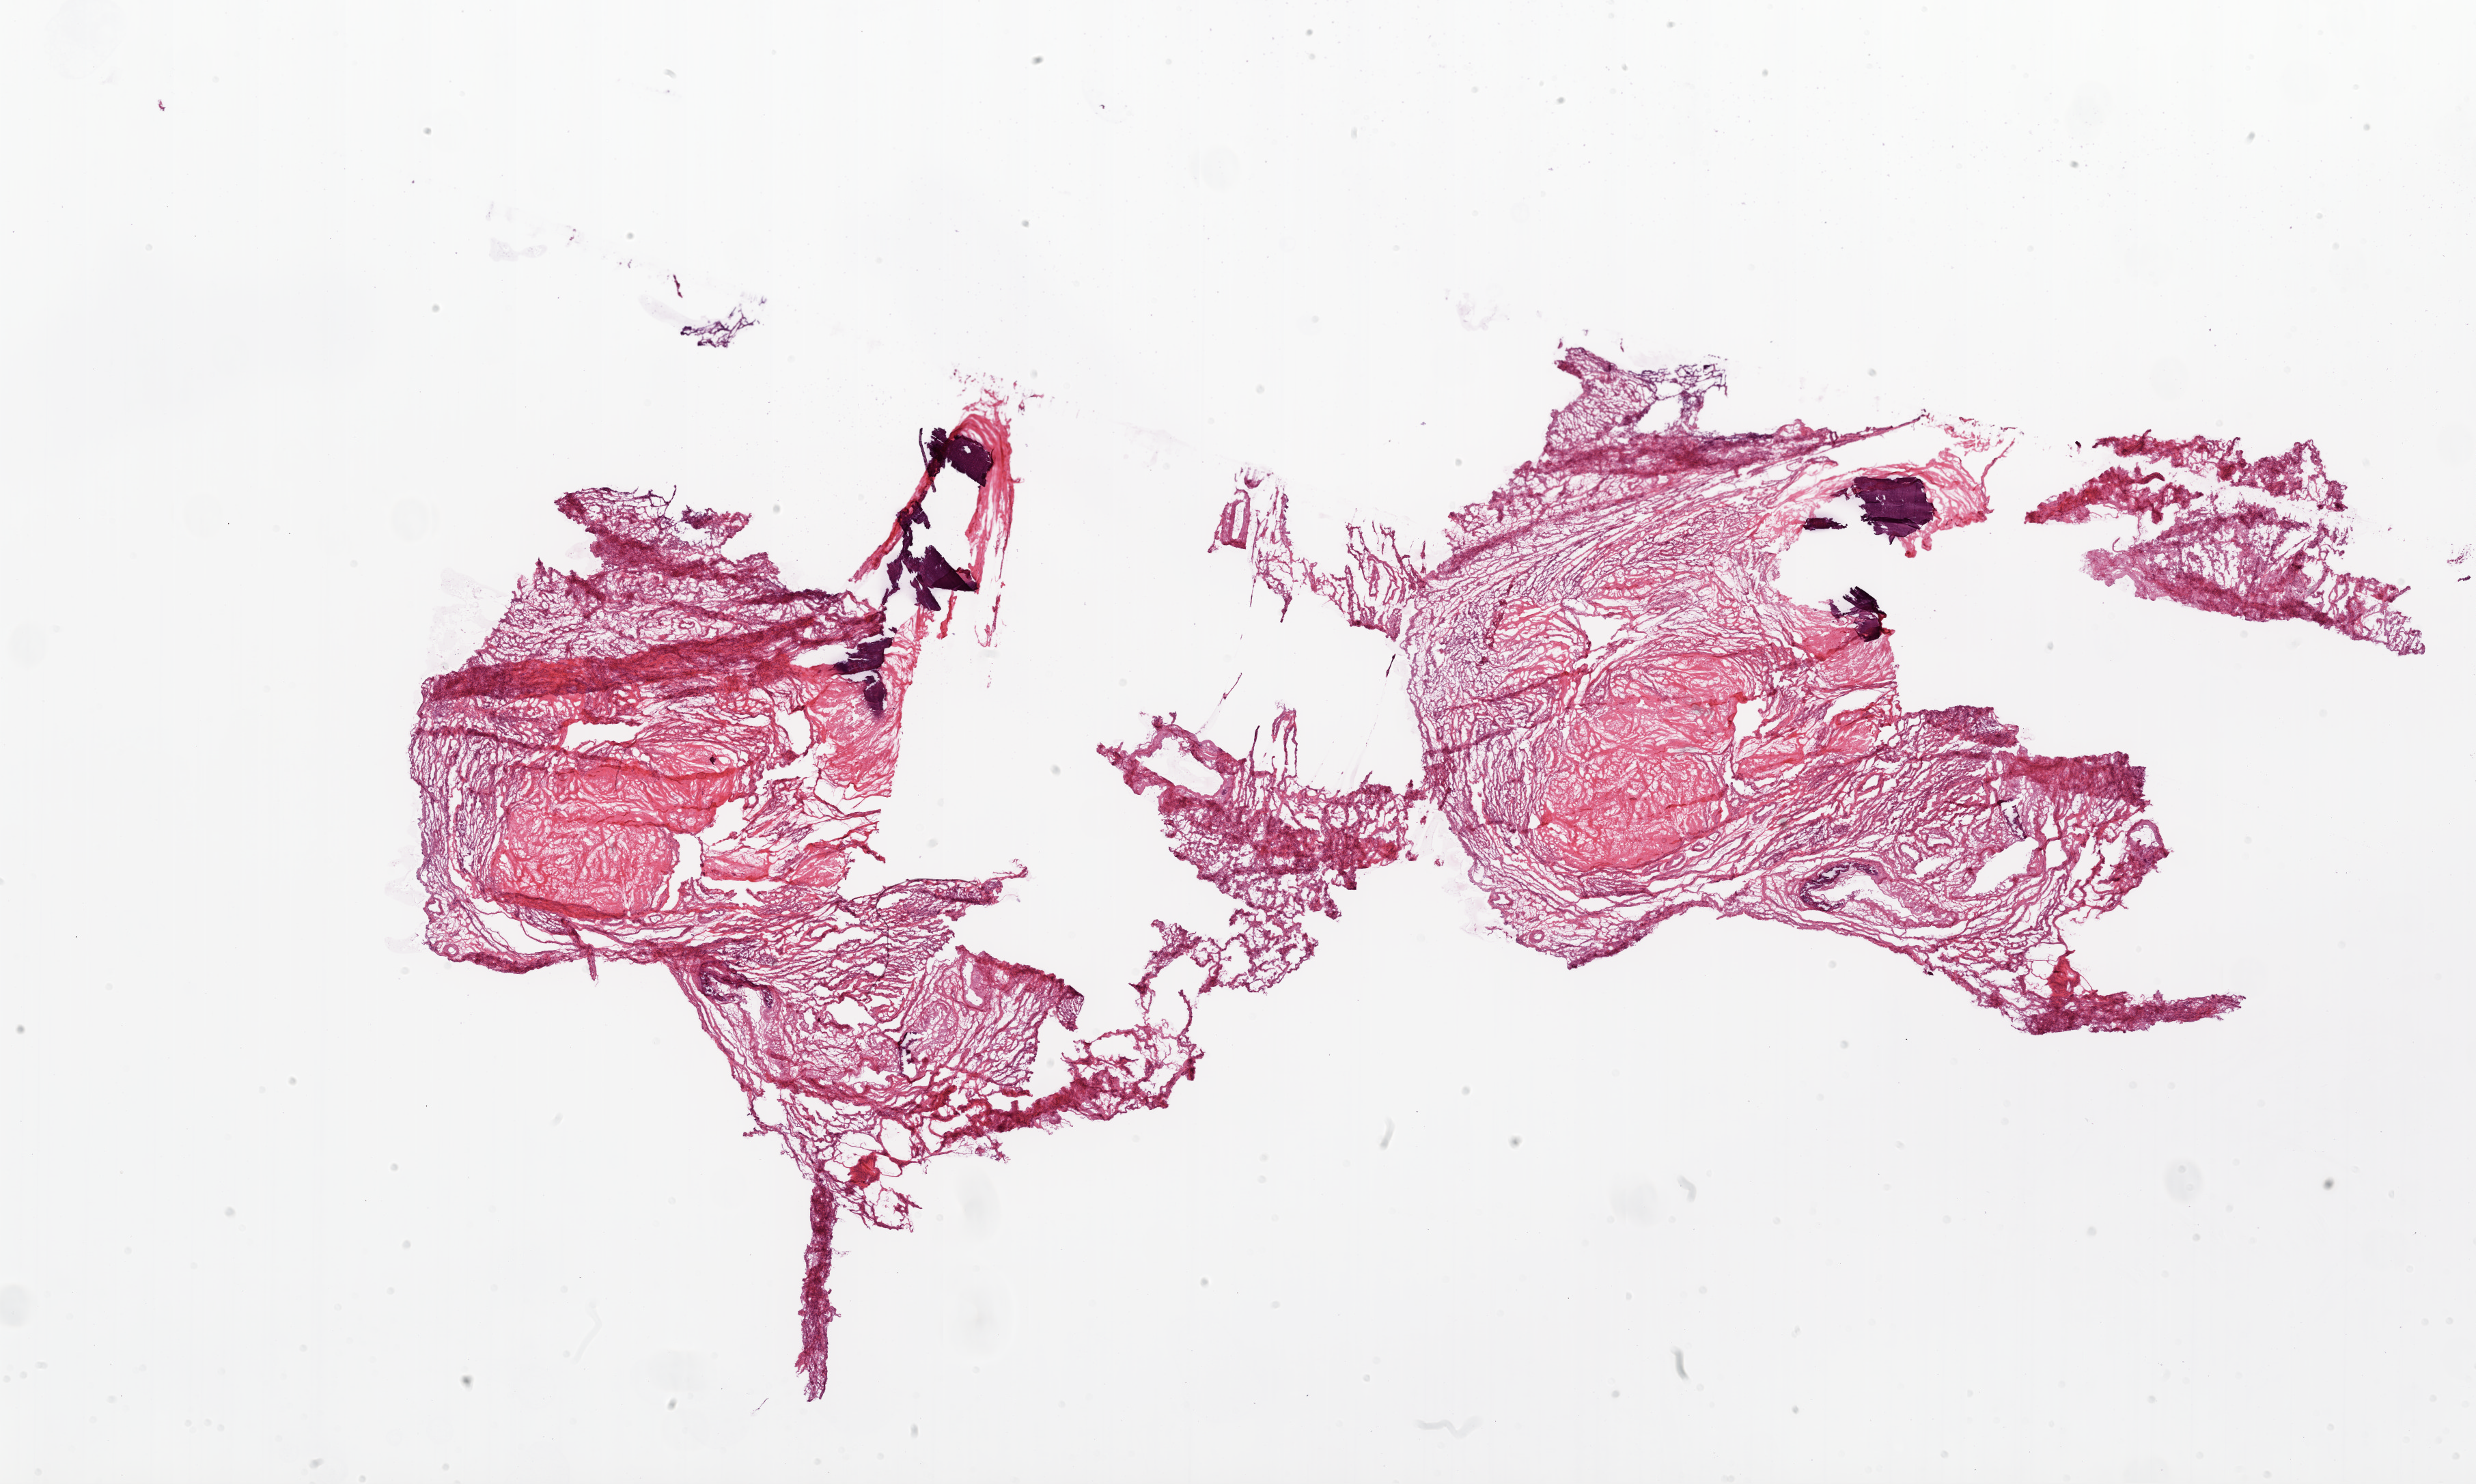
H&E-stained whole-slide image, a low-resolution overview of the entire scanned area, about 29.1 x 17.4 mm; frozen section from the top of the tissue portion; sample: solid tissue normal (non-tumour tissue), ovary. Female patient; age at initial diagnosis 72 years.
This section: solid tissue normal sample (biorepository sample class). Patient diagnosis: Serous cystadenocarcinoma, NOS.